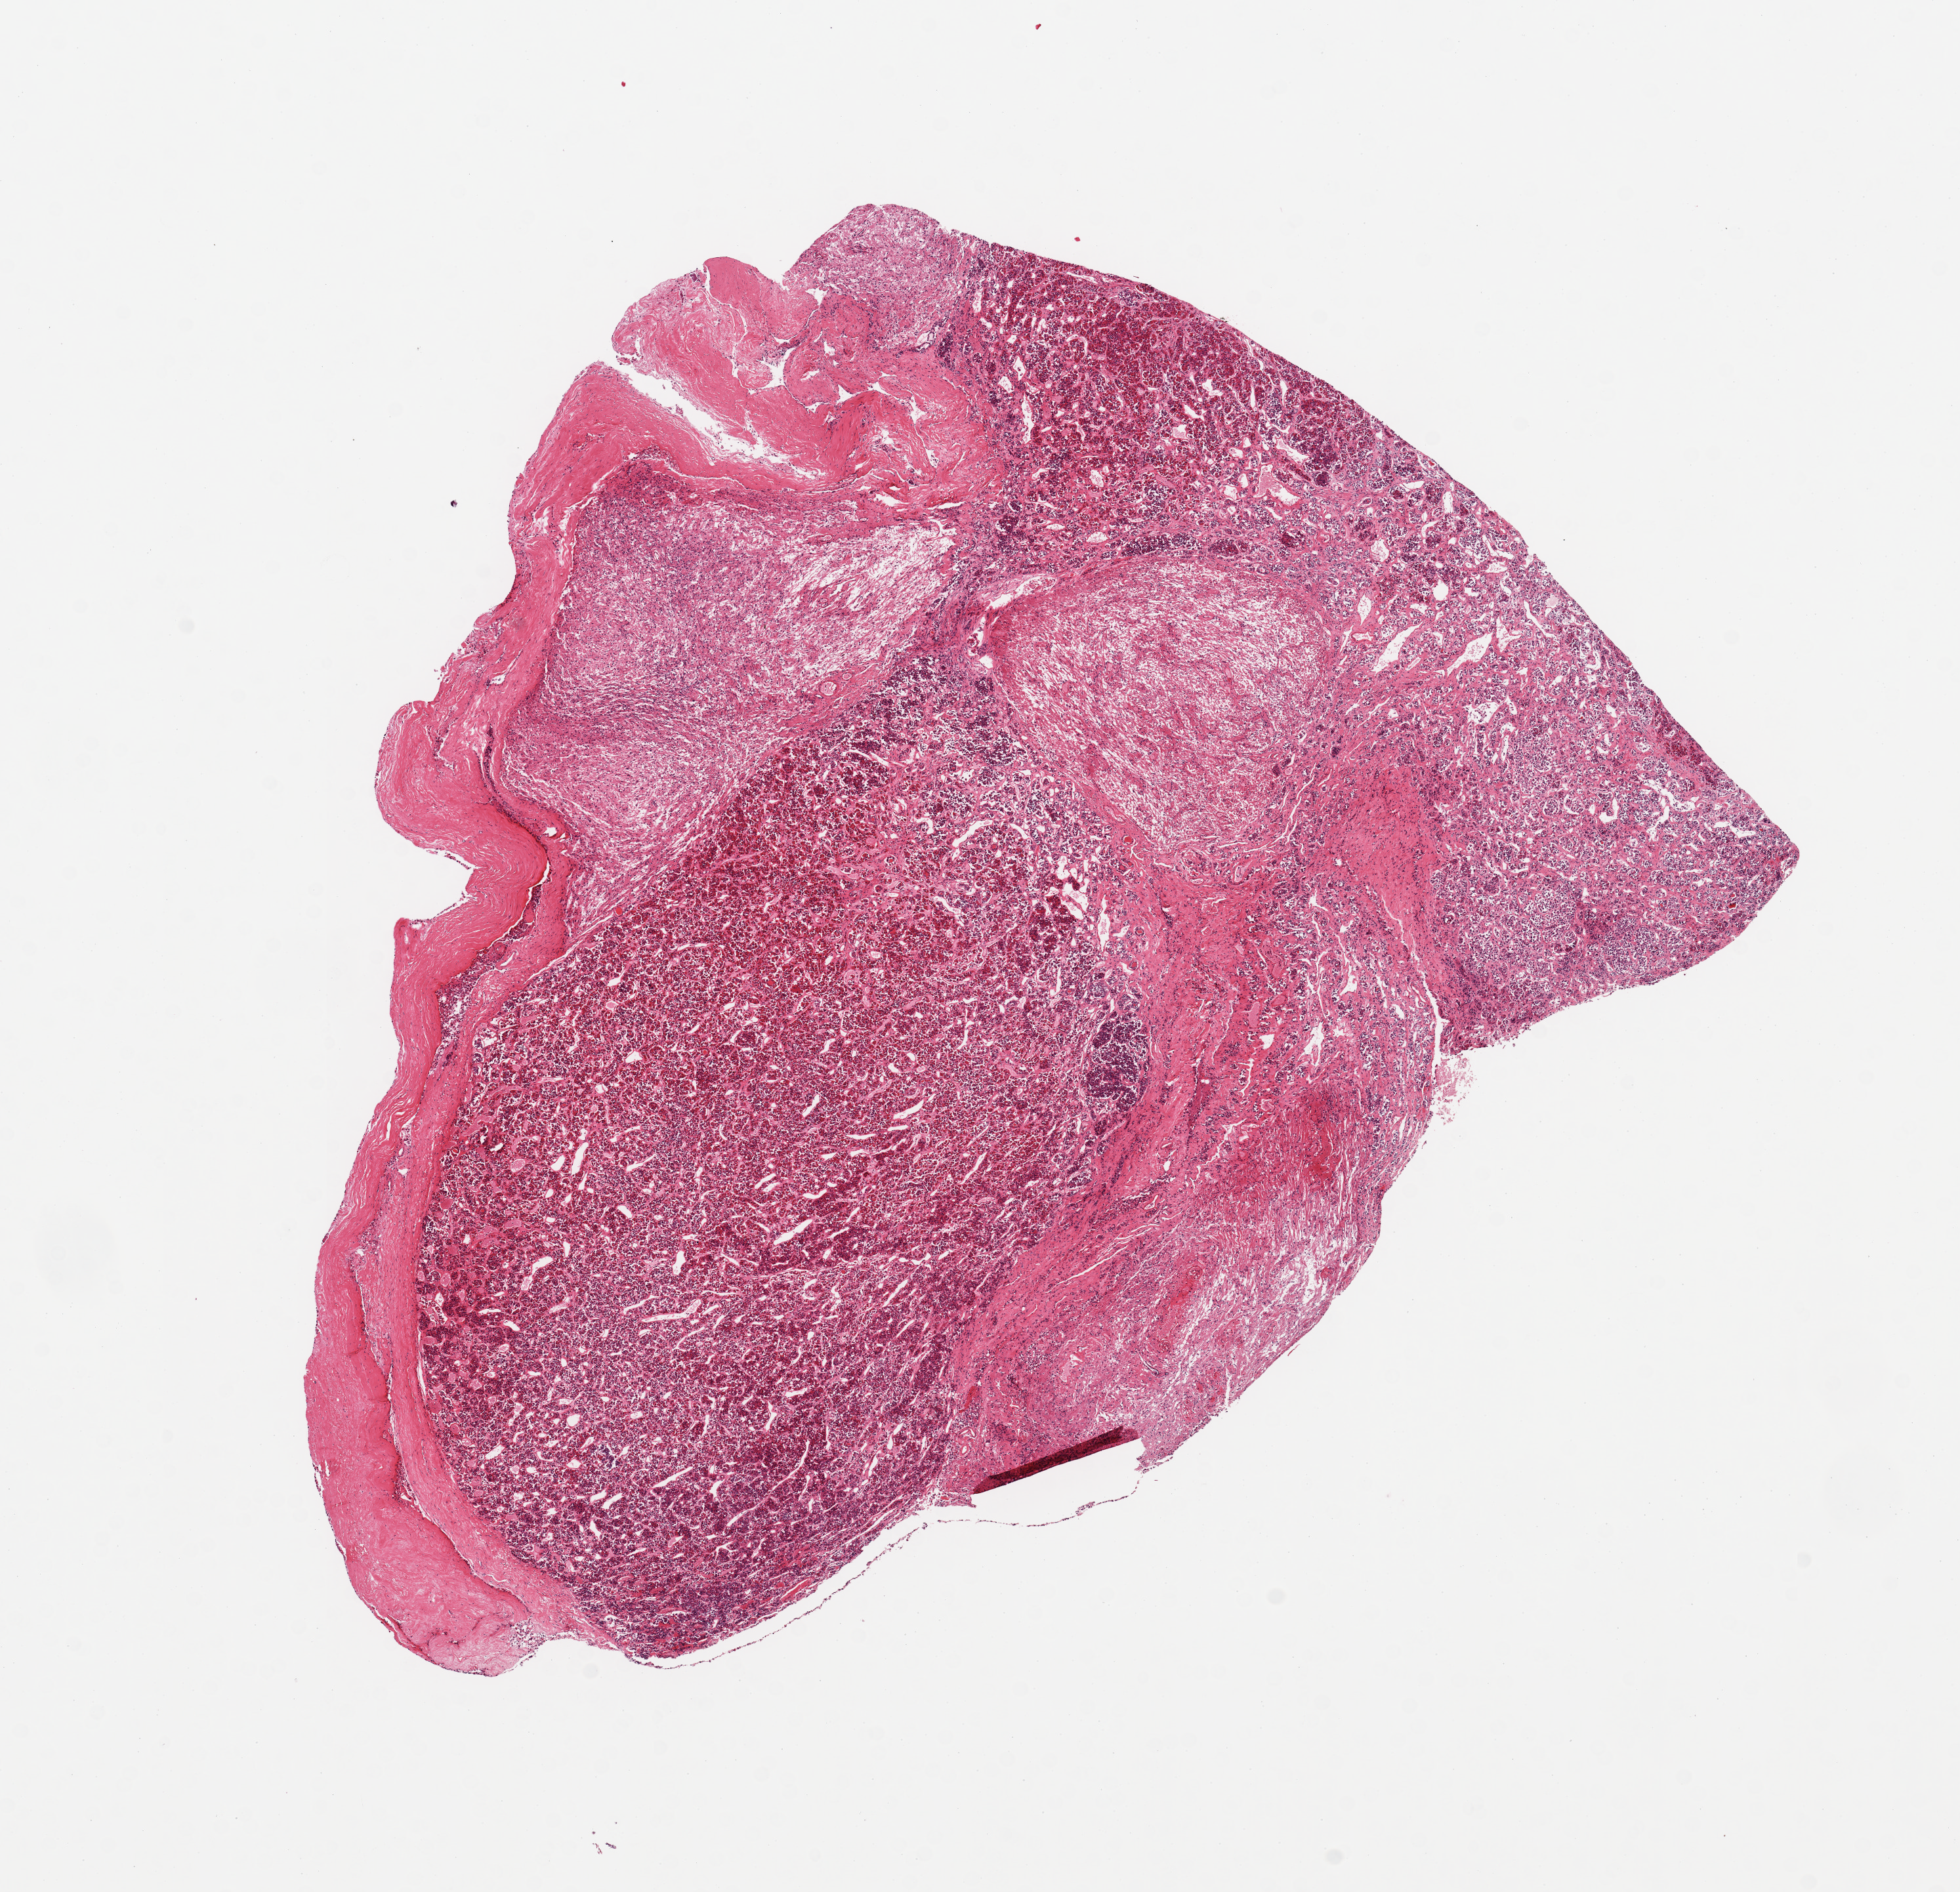
Haematoxylin and eosin whole-slide image — low-resolution overview of the scanned area, about 11.8 x 11.4 mm; PAXgene-fixed paraffin-embedded (PFPE) section; section of pituitary (target tissue); donor tissue sample. Donor sex: female.
Reviewer comment on this tissue sample: 1 piece; neurohypophysis makes up about 30%.